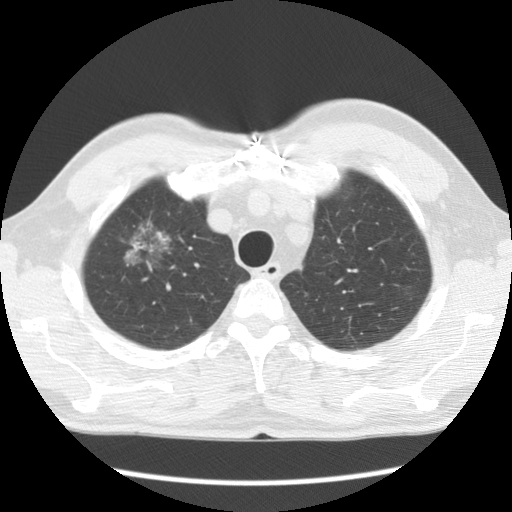
Low-dose screening chest CT, axial slice, baseline annual screen, lung window (W 1500 / L -600 HU), 2.5 mm slice thickness, standard (soft-tissue) reconstruction kernel (STANDARD), 120 kVp, 512 × 512 image matrix. Male, age 64 years at enrolment. Former smoker at enrolment.
- Expert-annotated lung lesion, box from (x=100, y=201) to (x=177, y=276) px.
- The screening reader recorded 2 non-calcified nodules or masses ≥4 mm on this exam (right upper lobe, left upper lobe); which of them this box marks is not recorded.
- Lung cancer was diagnosed 750 days after this screen: adenocarcinoma, NOS, right upper lobe, well differentiated (G1), stage IB (AJCC 6th edition), 45 mm at pathology.